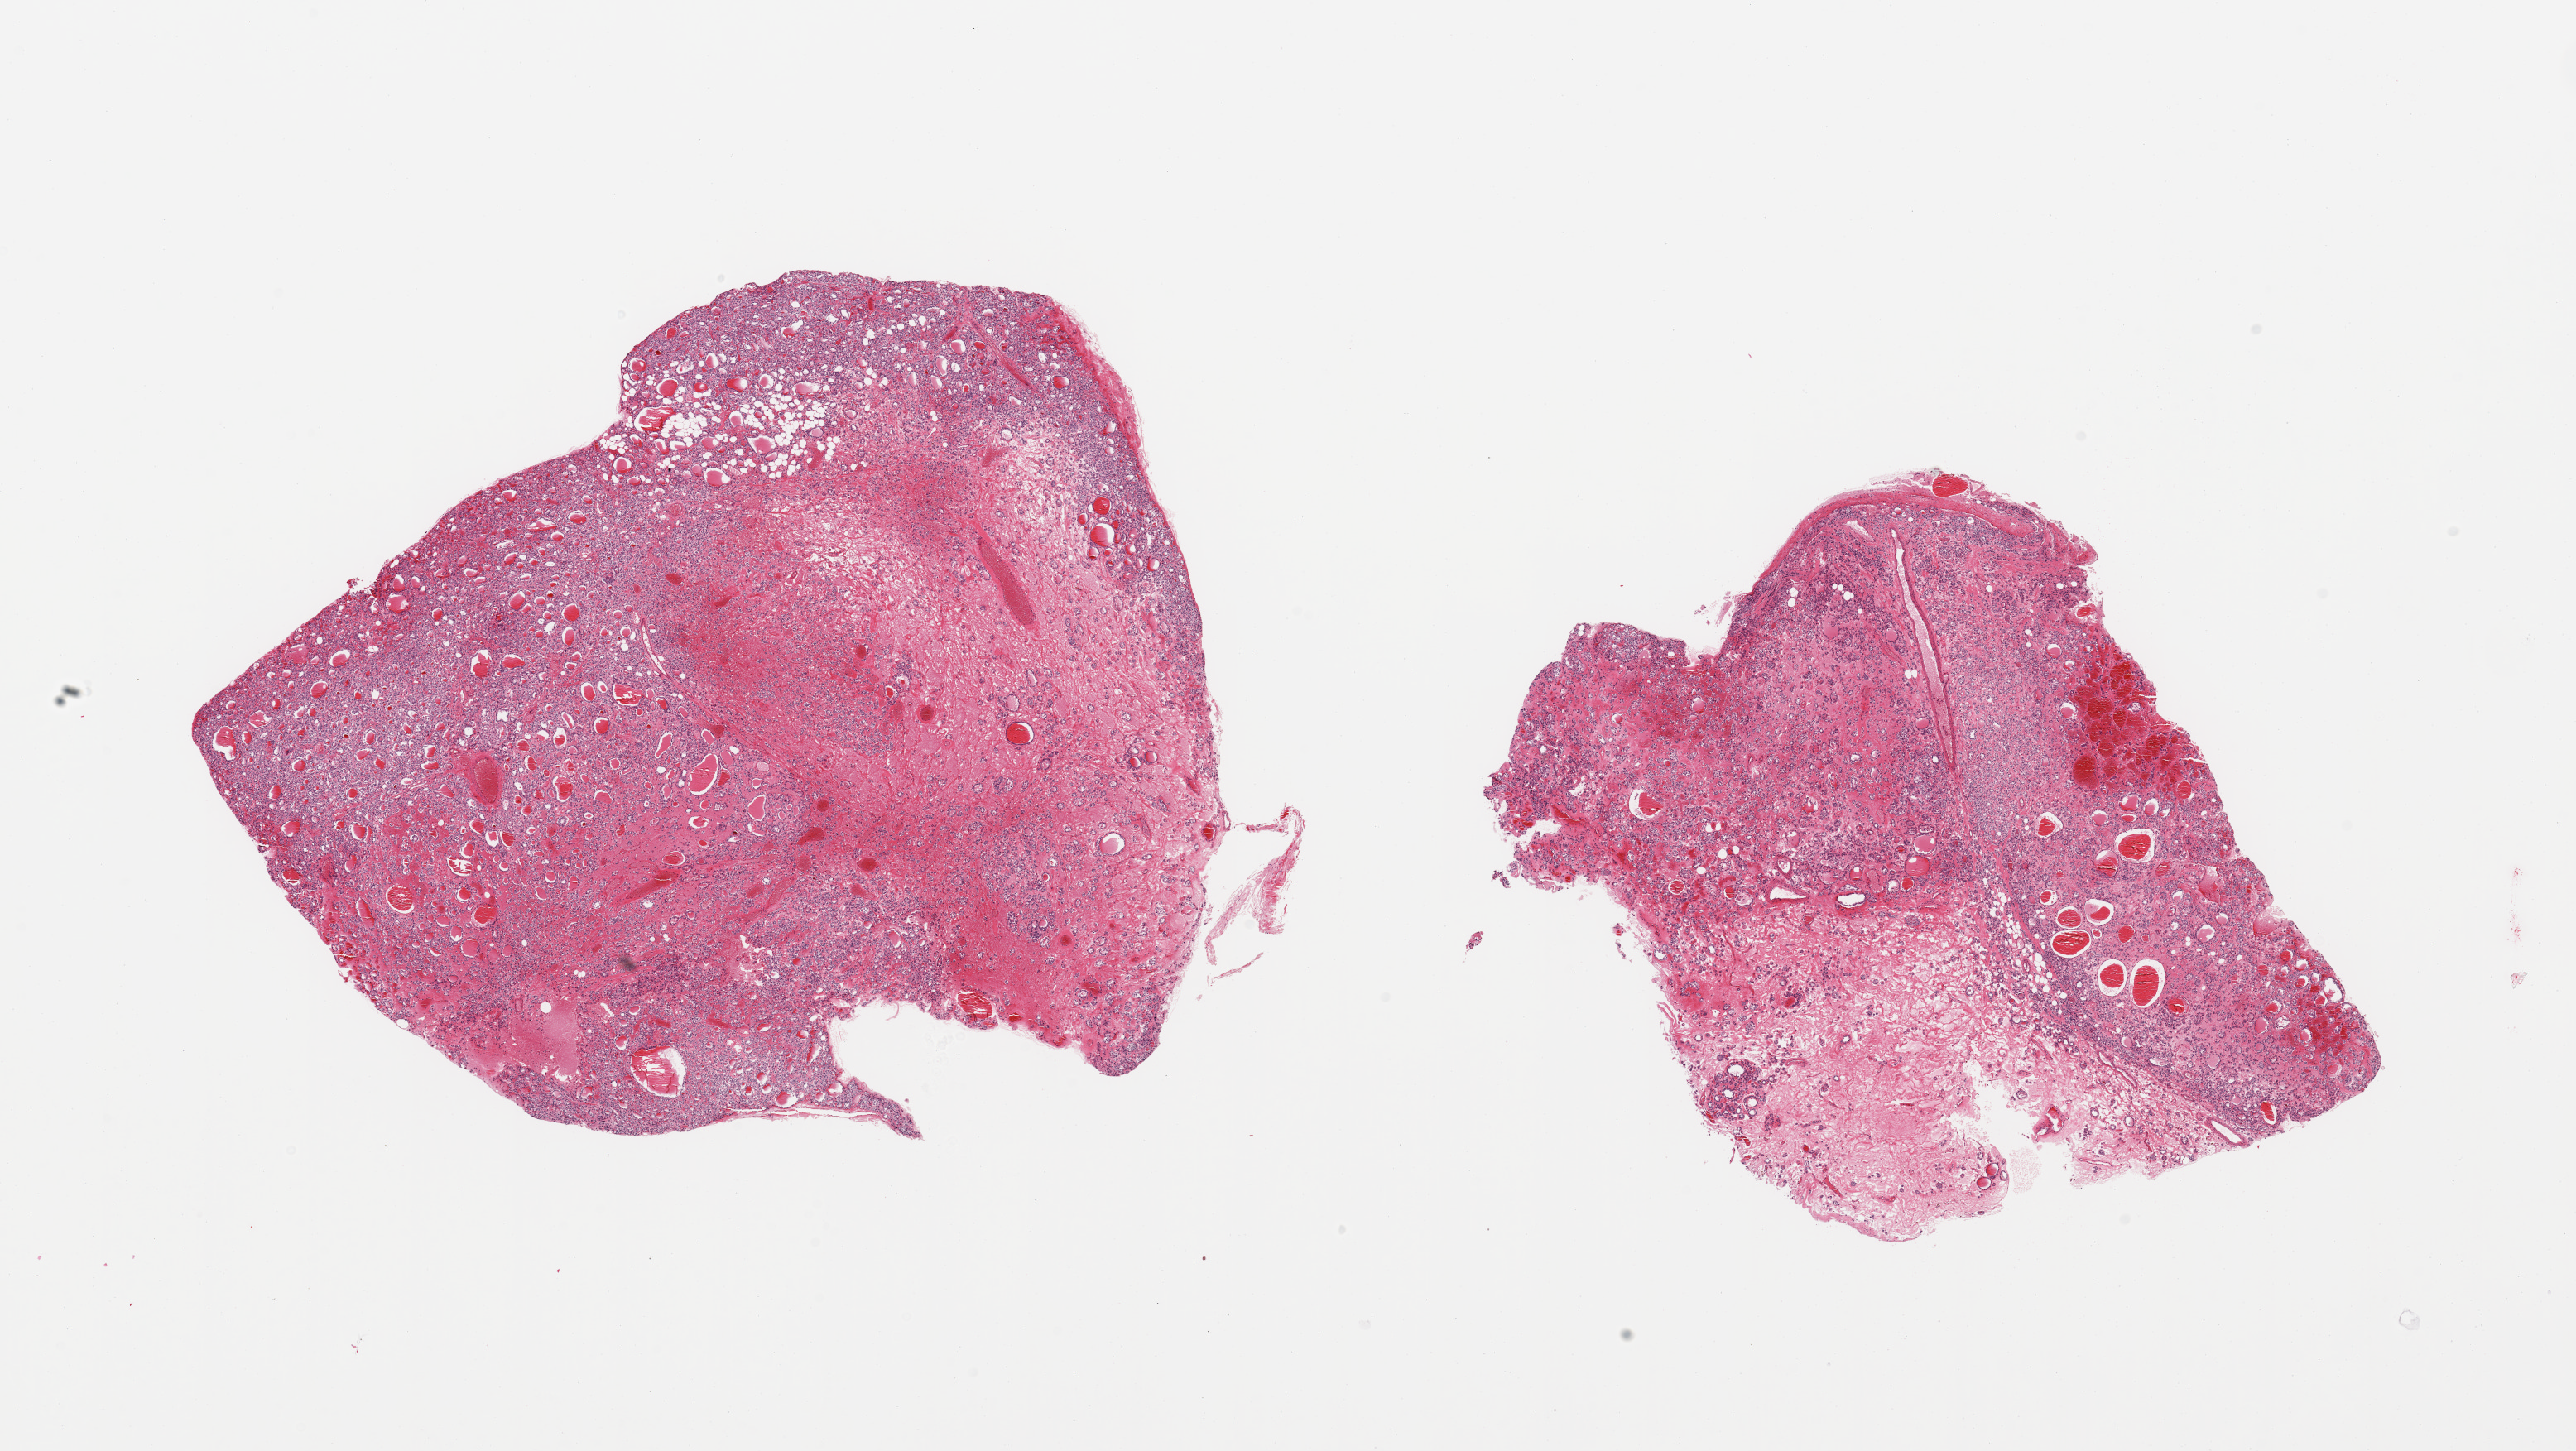
Whole-slide image, haematoxylin and eosin stain, a low-resolution overview of the entire scanned area, about 24.6 x 13.9 mm. Donor: male.
Specimen: PAXgene-fixed, paraffin-embedded tissue; target tissue: thyroid; donor tissue sample.